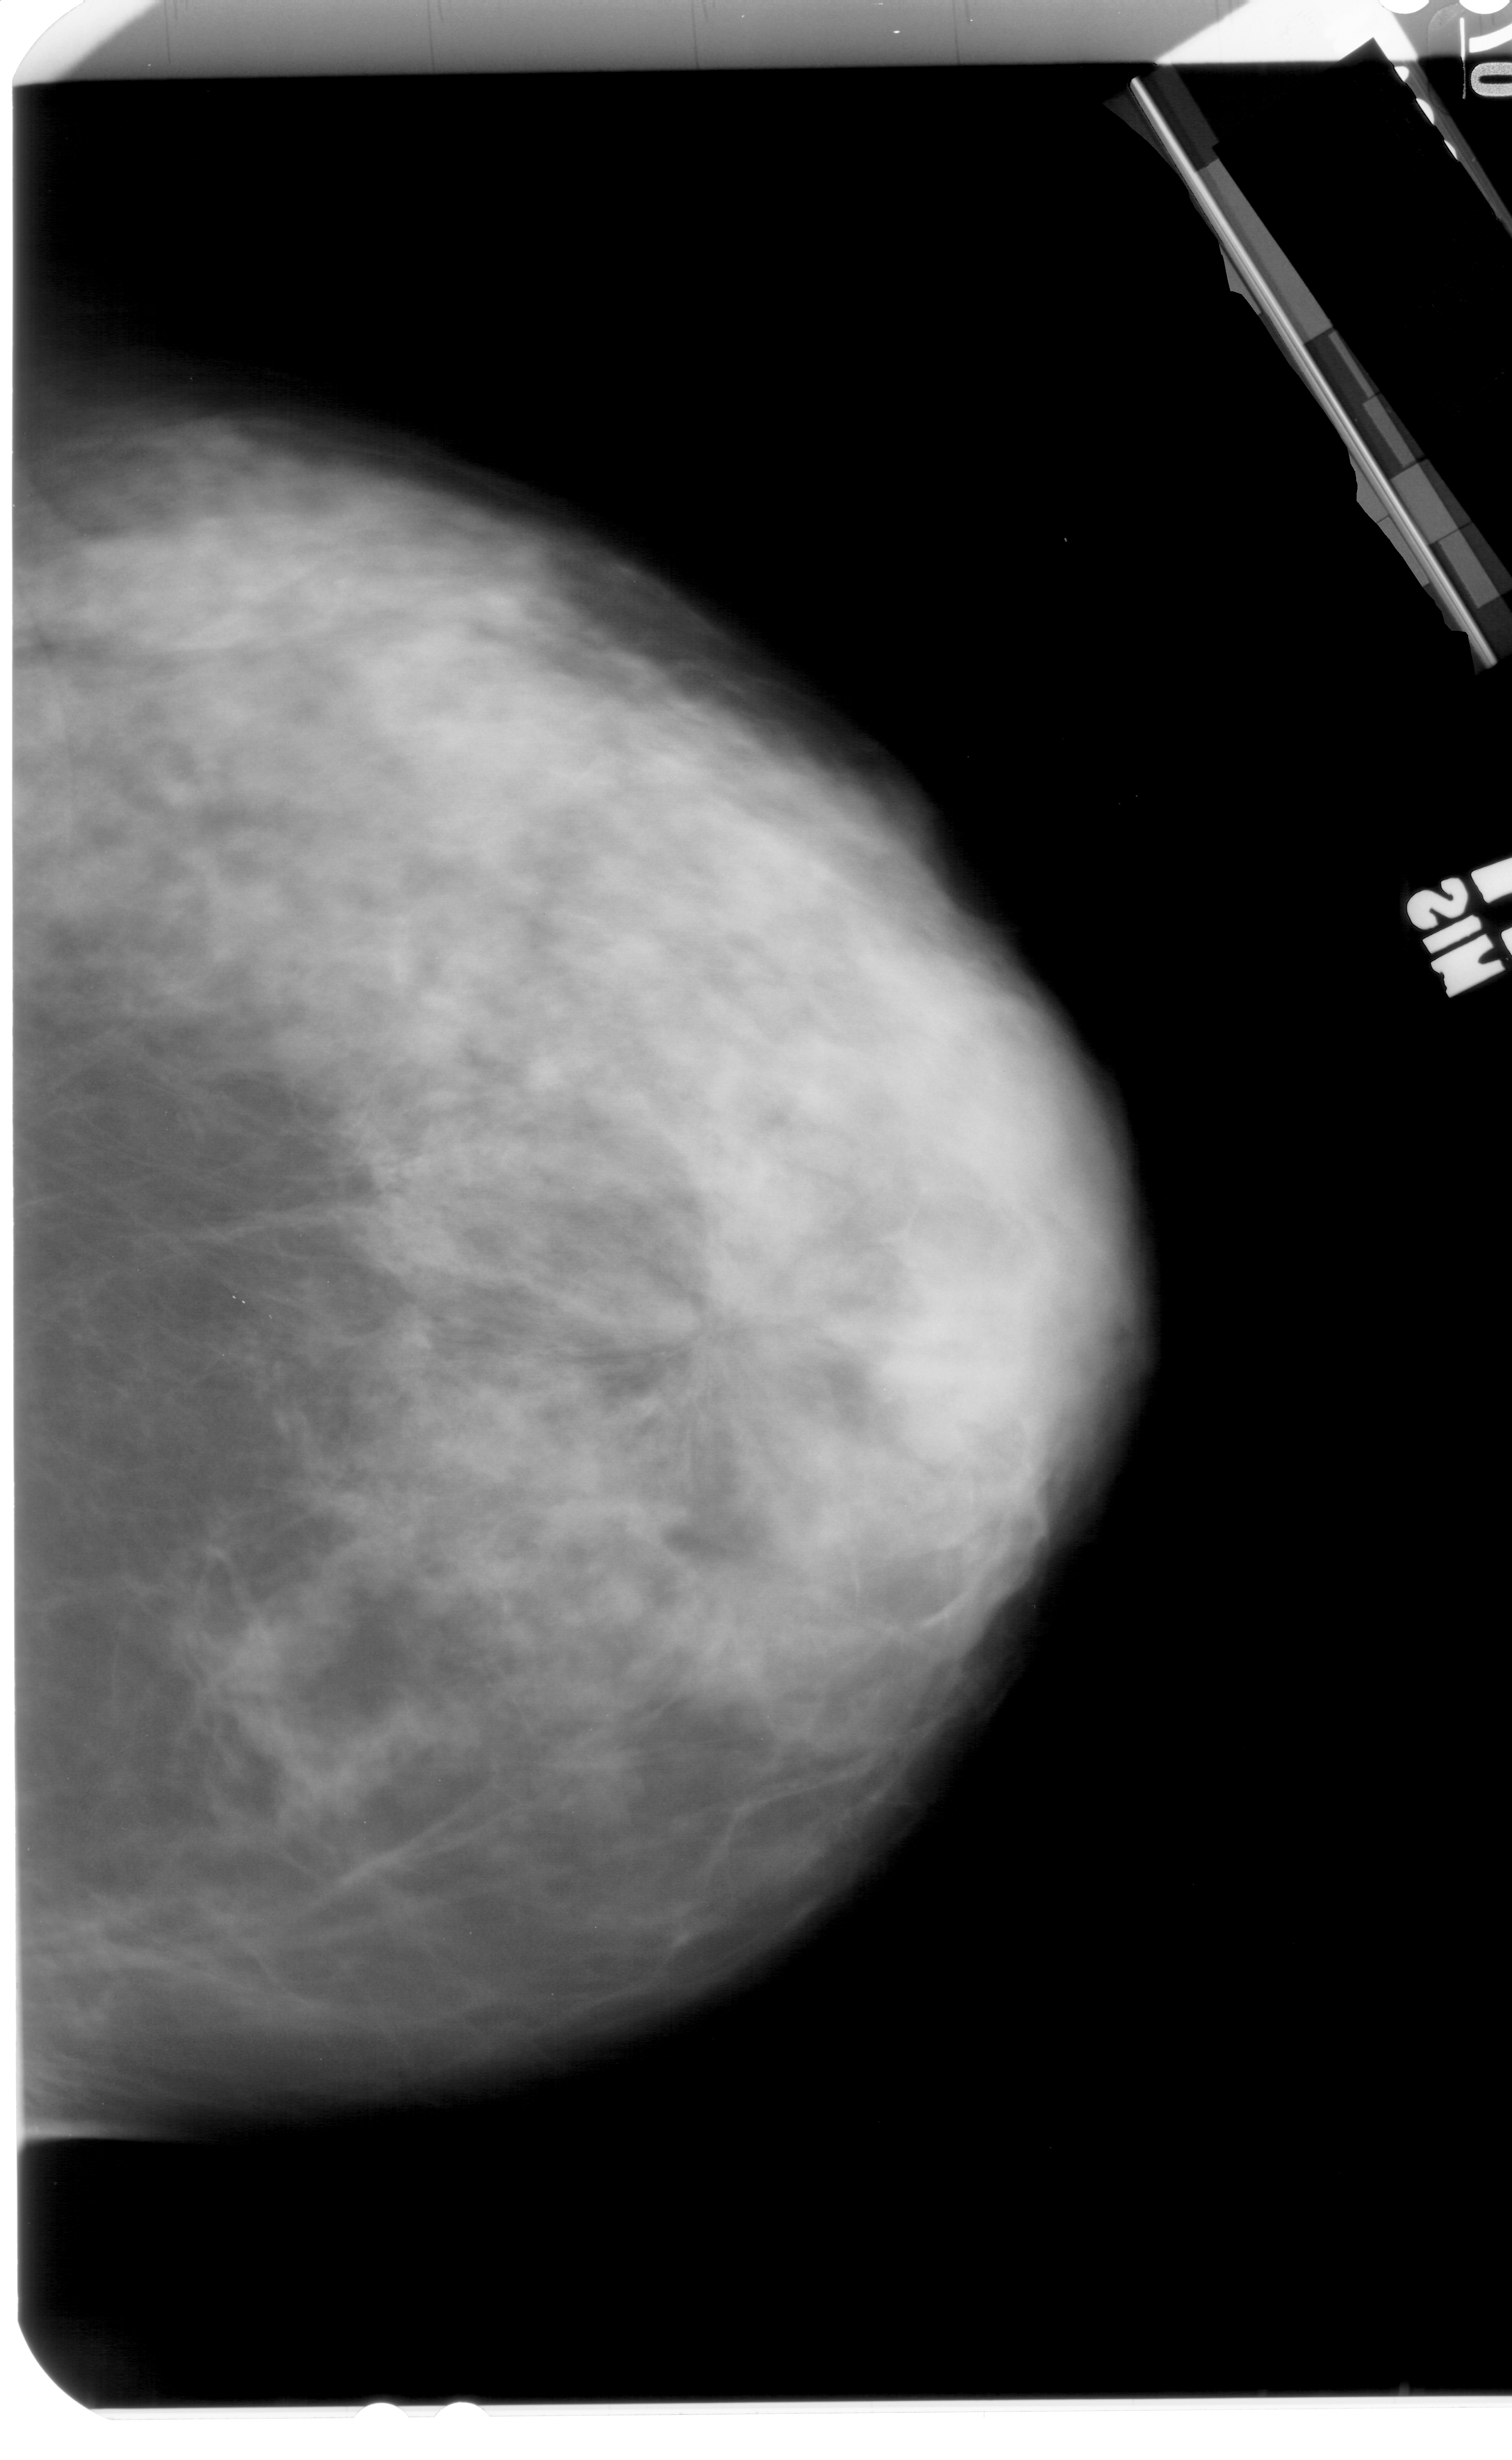
Digitized screen-film mammogram; right breast; CC view; breast composition: extremely dense (BI-RADS density category 4 of 4).
Radiologist-marked abnormalities on this image: mass, shape architectural distortion, margins spiculated; BI-RADS assessment category 5; pathology result (as recorded, not read from the image): malignant.